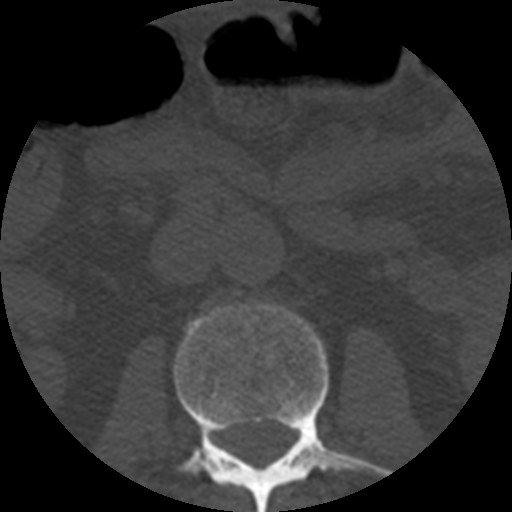
CT including the spine, one axial slice. Position 150 of 508 along the scan axis. Reconstruction kernel STANDARD. 120 kVp. Bone window (W 1800 / L 400 HU). 1.25 mm slice thickness. 512 × 512 image matrix, field of view 160 × 160 mm. Patient age 57 years. Case-level facts recorded for this patient, not image findings: primary cancer: prostate.
Structures marked on this image (semi-automatic segmentation, software-assisted and operator-edited):
- L2 vertebra: bounding box (x1, y1, x2, y2) in pixels: (174, 304, 389, 512)